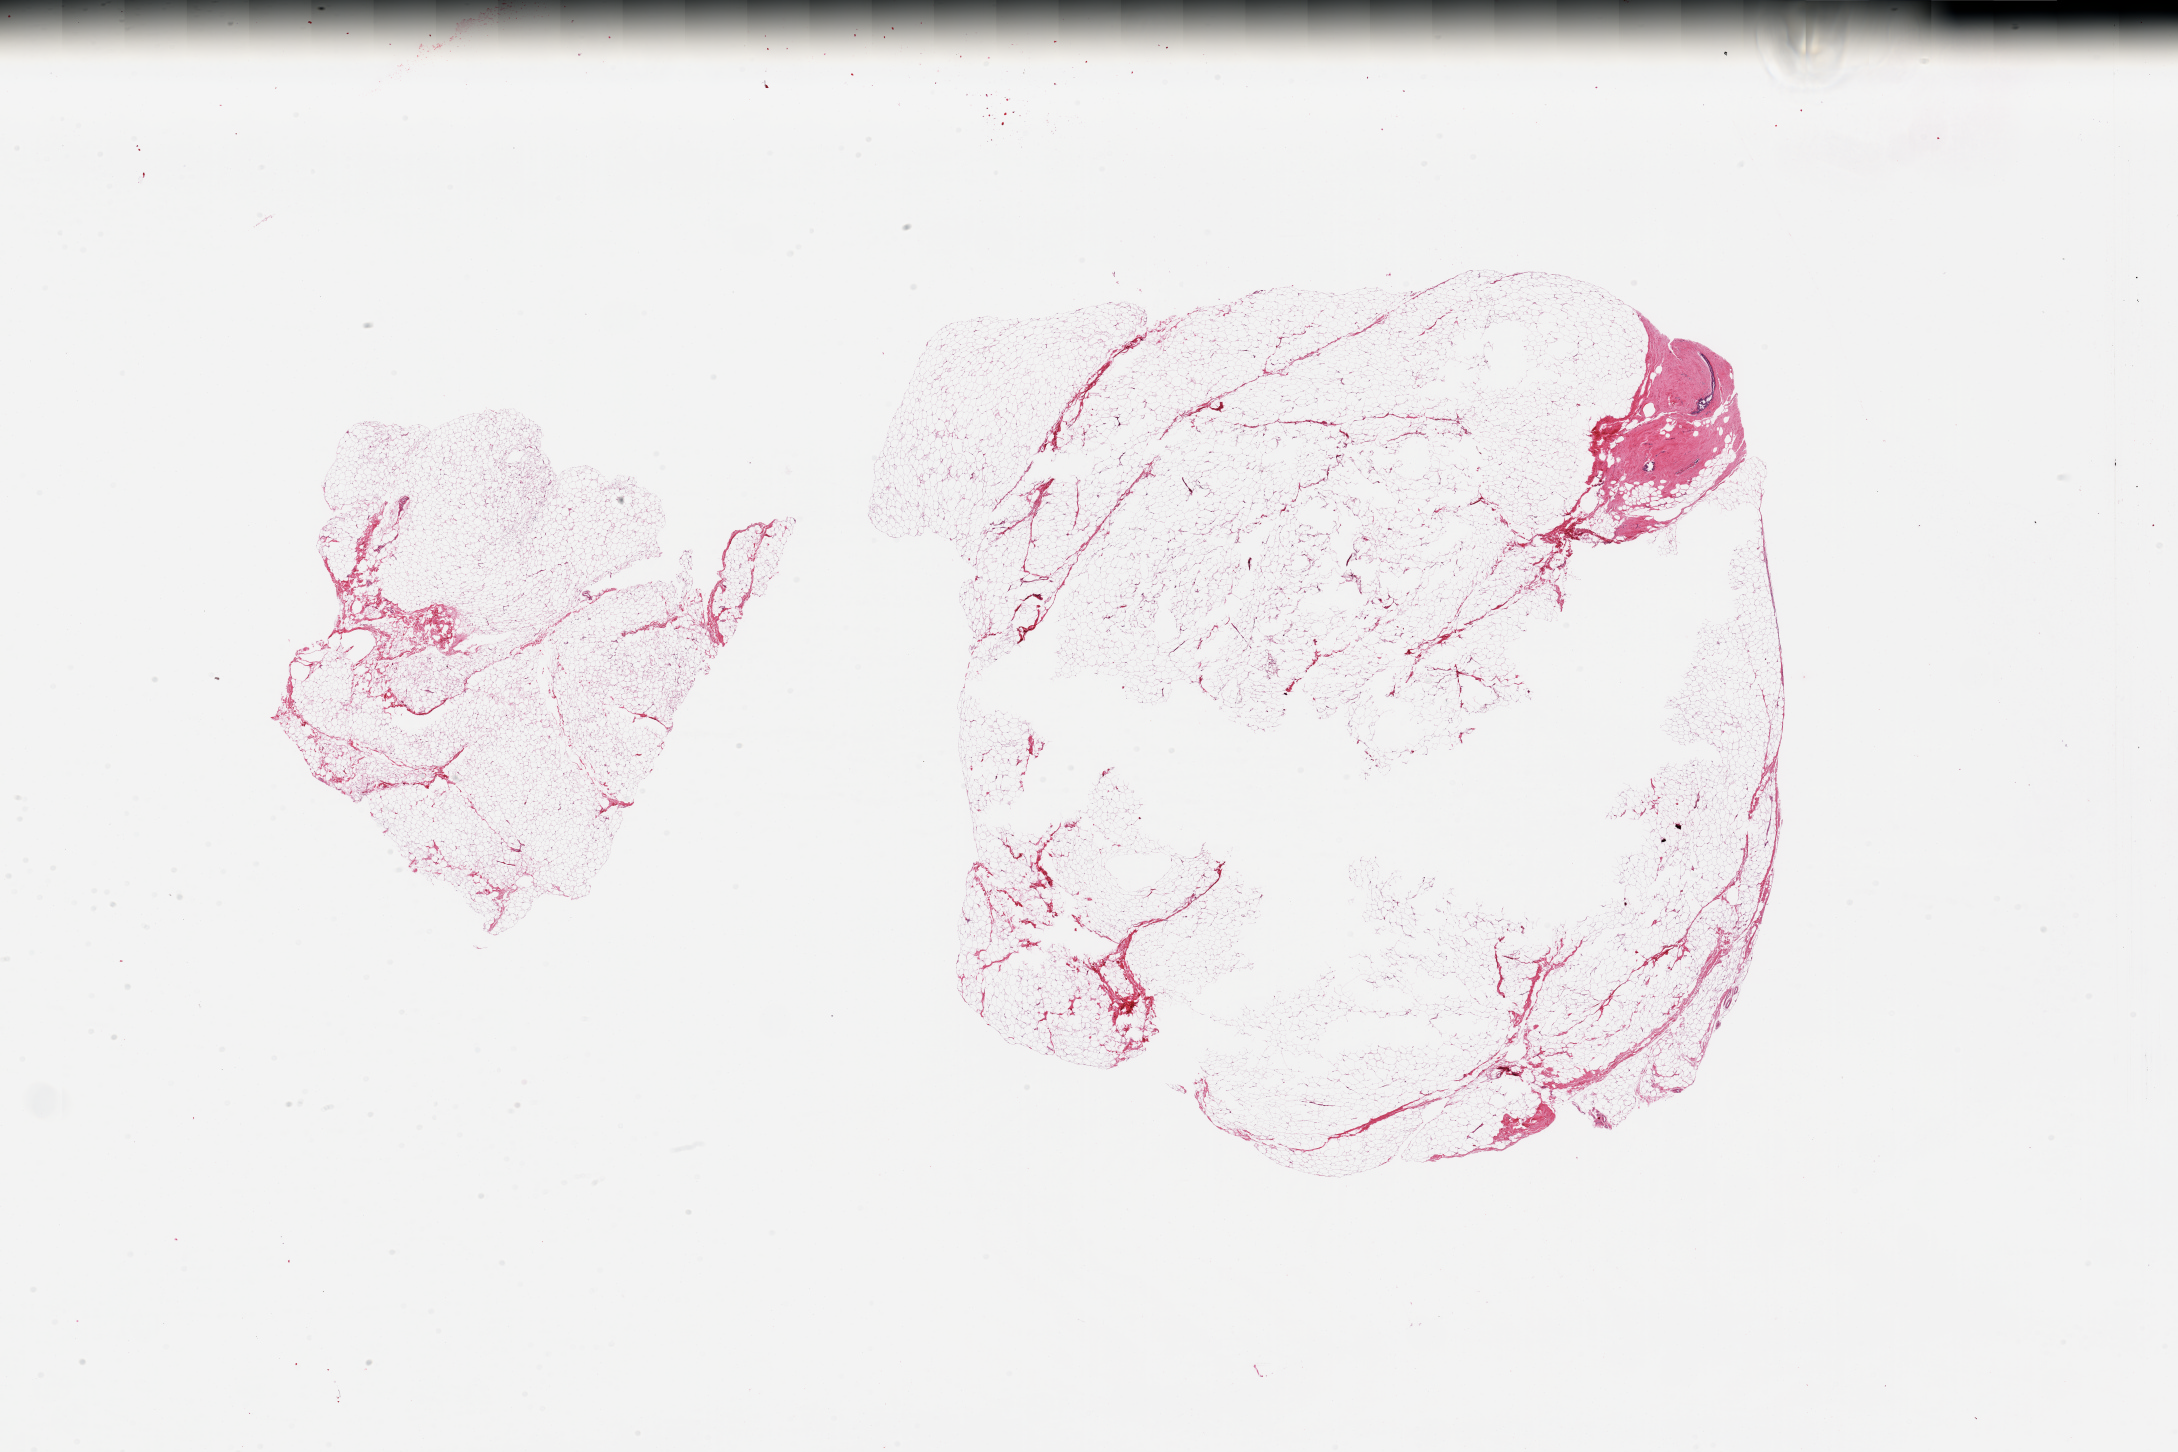
Digitized H&E-stained section, brightfield — shown as a low-resolution overview of the whole scanned area (about 34.5 x 23.0 mm), PAXgene-fixed paraffin-embedded (PFPE) section, section of breast (target tissue), tissue donor sample. Male donor.
Review note (as recorded): 2 pieces; 90% adipose; a 2mm fibrous focus with several mammary ducts.